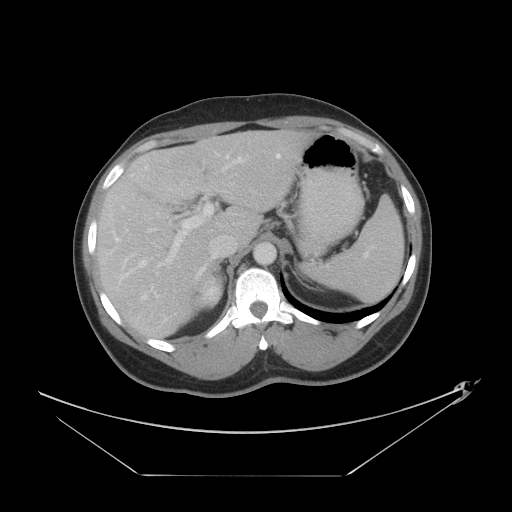
Contrast-enhanced abdominal CT, one axial slice. Position 28 of 44 along the scan axis. Reconstruction kernel STANDARD. 120 kVp. Intravenous contrast given. Soft-tissue window (W 400 / L 40 HU). 5 mm slice thickness. 512 × 512 image matrix. Male patient, age 49 years. From the clinical record (not read from this slice): diagnosis: colorectal cancer liver metastases, imaged before liver resection; multiple liver metastases: no; largest metastasis: 8.5 cm; disease in both lobes: yes.
Annotated regions visible in this slice (expert manual segmentation):
- hepatic veins: bounding box (x1, y1, x2, y2) in pixels: (140, 154, 280, 274)
- liver: (96, 131, 317, 340)
- planned liver remnant (the part of the liver to remain after resection): (131, 131, 317, 246)
- portal vein (with intrahepatic branches): (115, 160, 245, 262)
- liver metastasis: (227, 168, 234, 173)